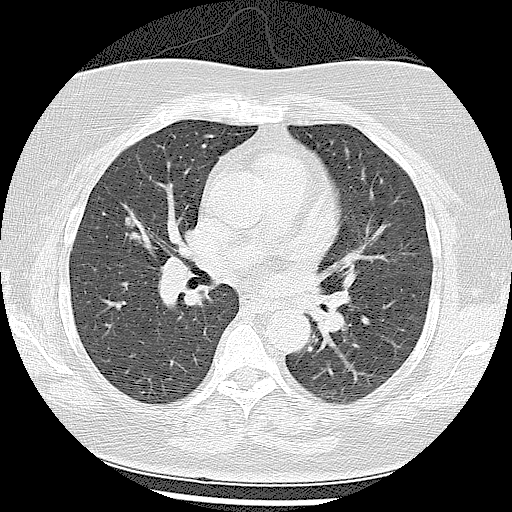
Low-dose screening chest CT, axial slice; first (baseline) screen; lung window (W 1500 / L -600 HU); 2.5 mm slice thickness; lung (sharp) reconstruction kernel (LUNG); 120 kVp; slice 49 of 102 in the series. Female, age 57 years at enrolment.
Expert-annotated lung lesion, bounding box [x1, y1, x2, y2] px = [103, 203, 168, 260]. The screening reader recorded 4 non-calcified nodules or masses ≥4 mm on this exam (right middle lobe, right lower lobe, left lower lobe, left lower lobe); which of them this box marks is not recorded. Official screen result: positive, change unspecified: nodule(s) >= 4 mm or enlarging nodule(s), mass(es), or other non-specific abnormalities suspicious for lung cancer. Lung cancer was diagnosed 87 days after this screen: adenocarcinoma, NOS, right middle lobe, well differentiated (G1), stage IA (AJCC 6th edition), 21 mm at pathology.